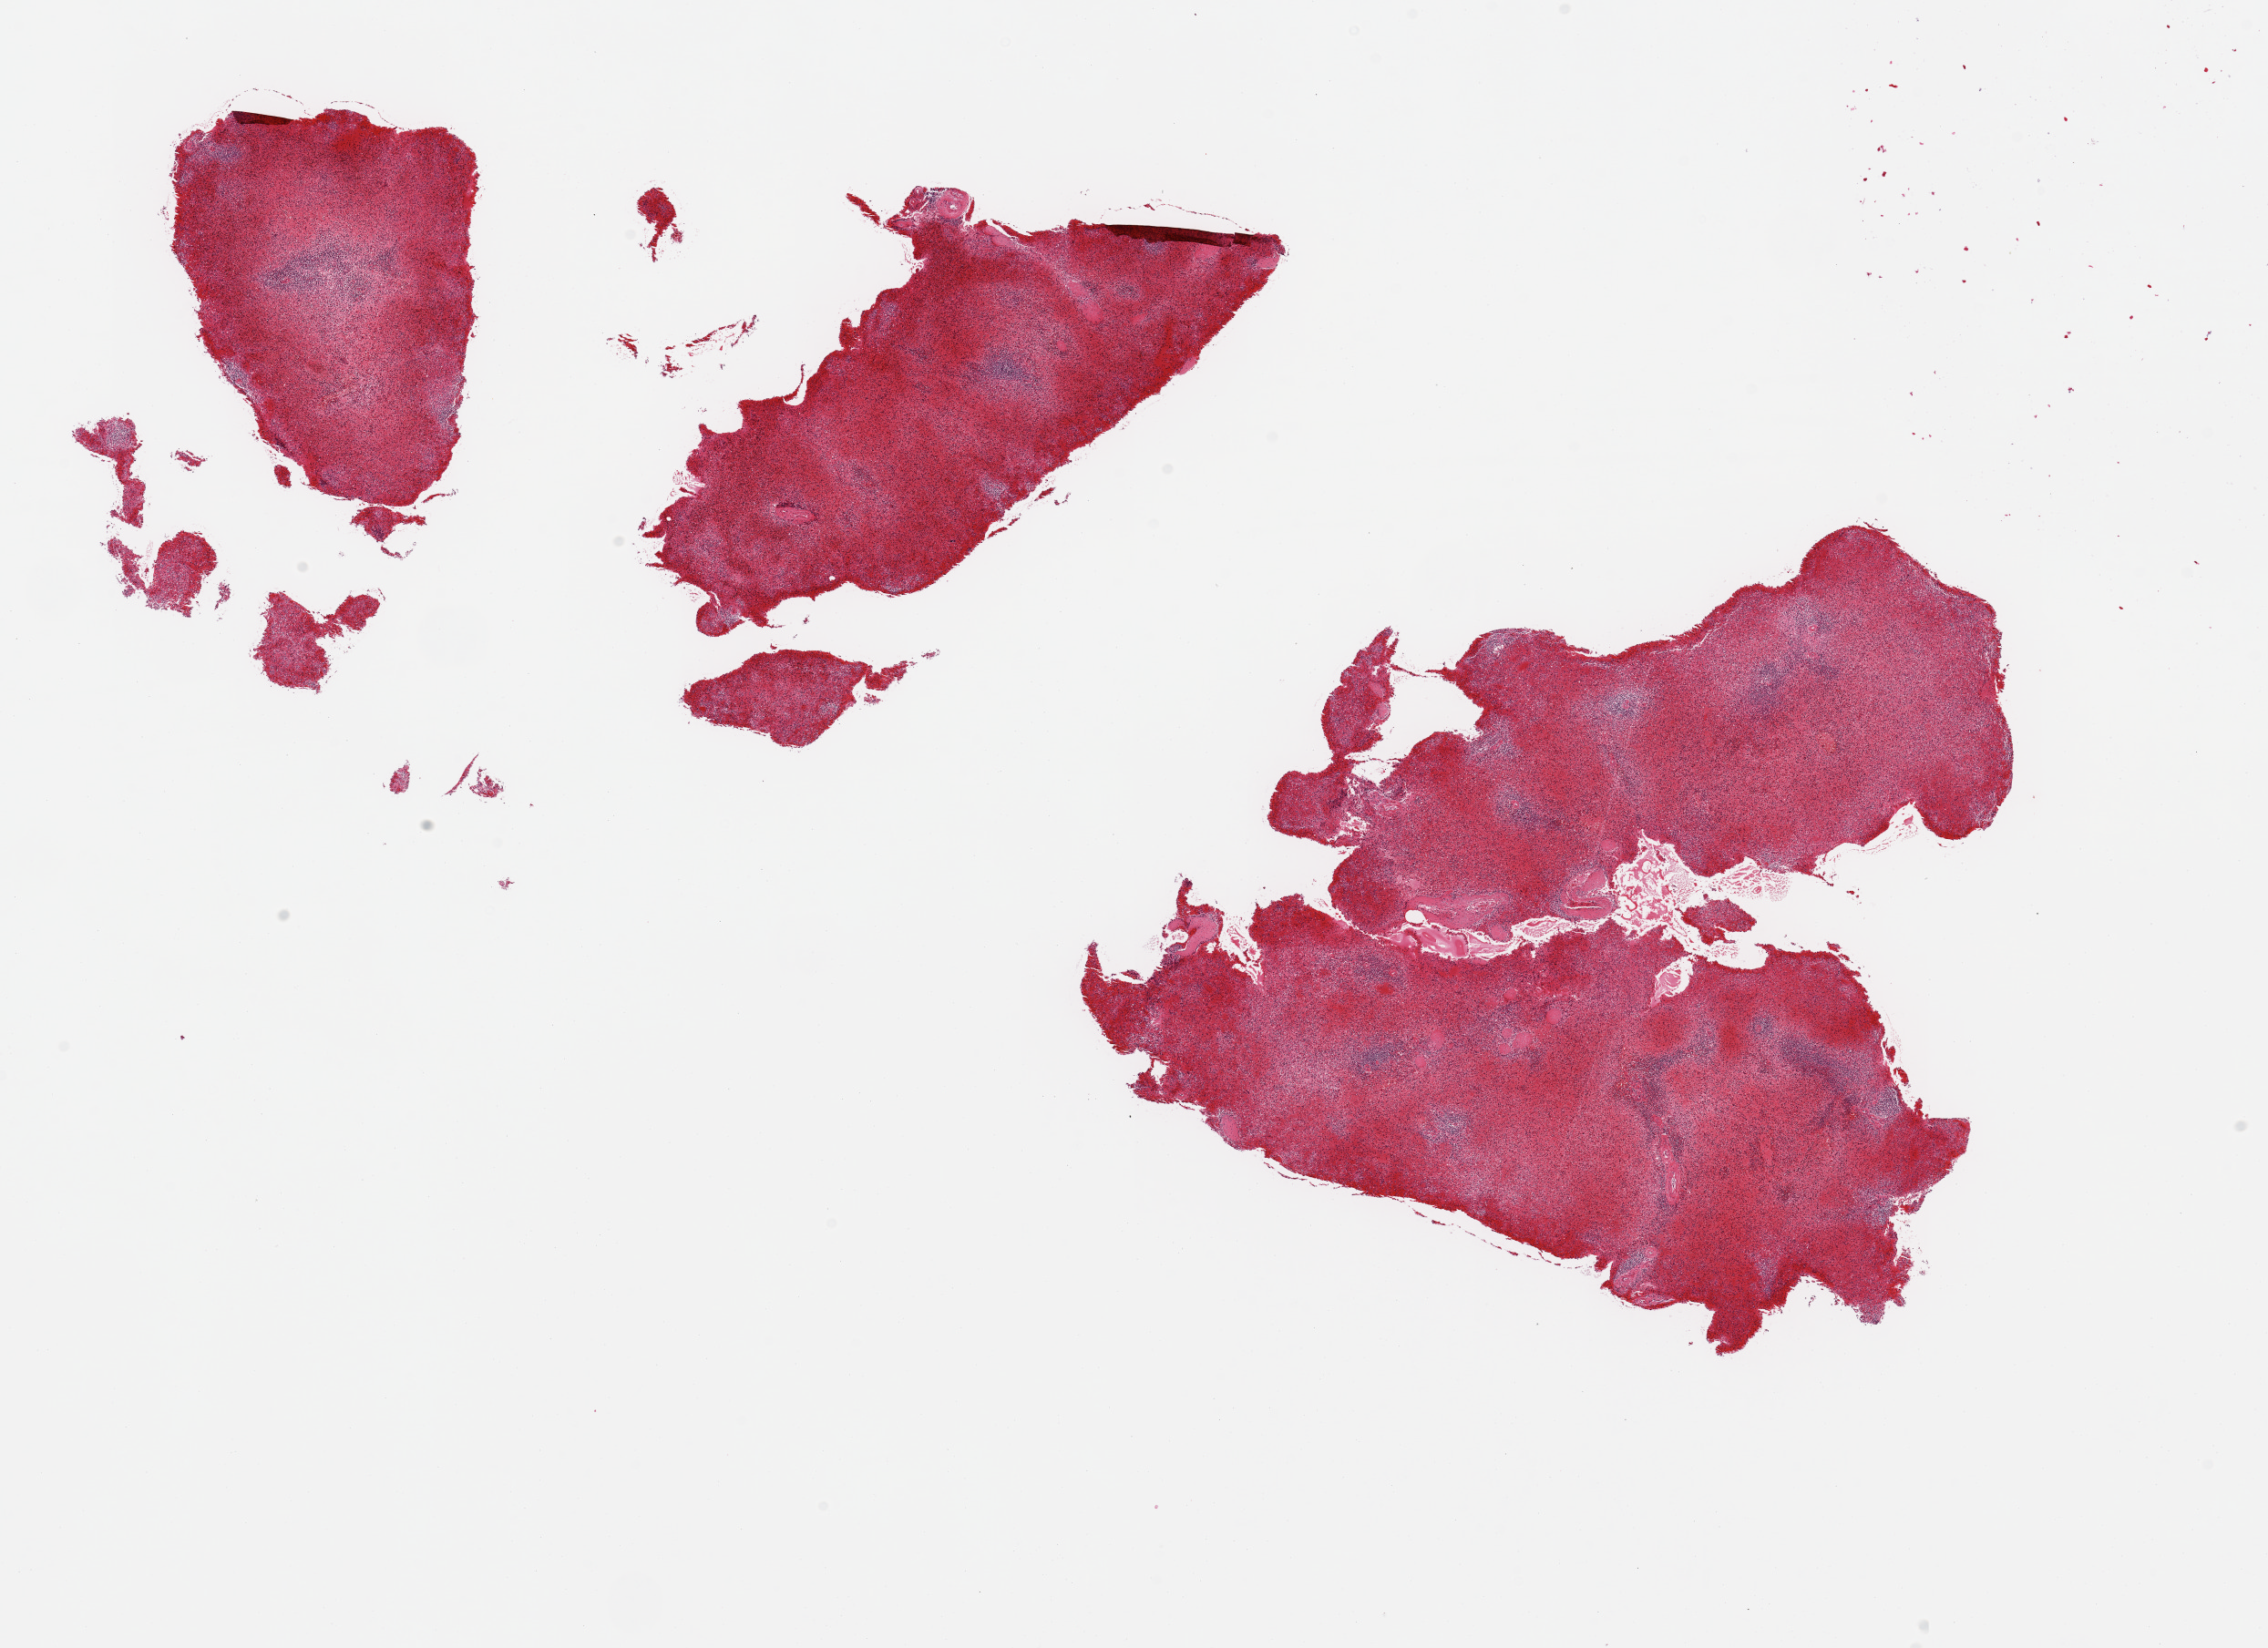
Whole-slide image, hematoxylin and eosin (H&E) stain, a low-resolution overview of the entire scanned area, about 19.7 x 14.3 mm (slide scanned at 20x); PAXgene-fixed paraffin-embedded (PFPE) section; section of spleen (target tissue); donor tissue sample. Donor: male.
Pathologist's review note for this sample: 2 pieces, marked congestion.